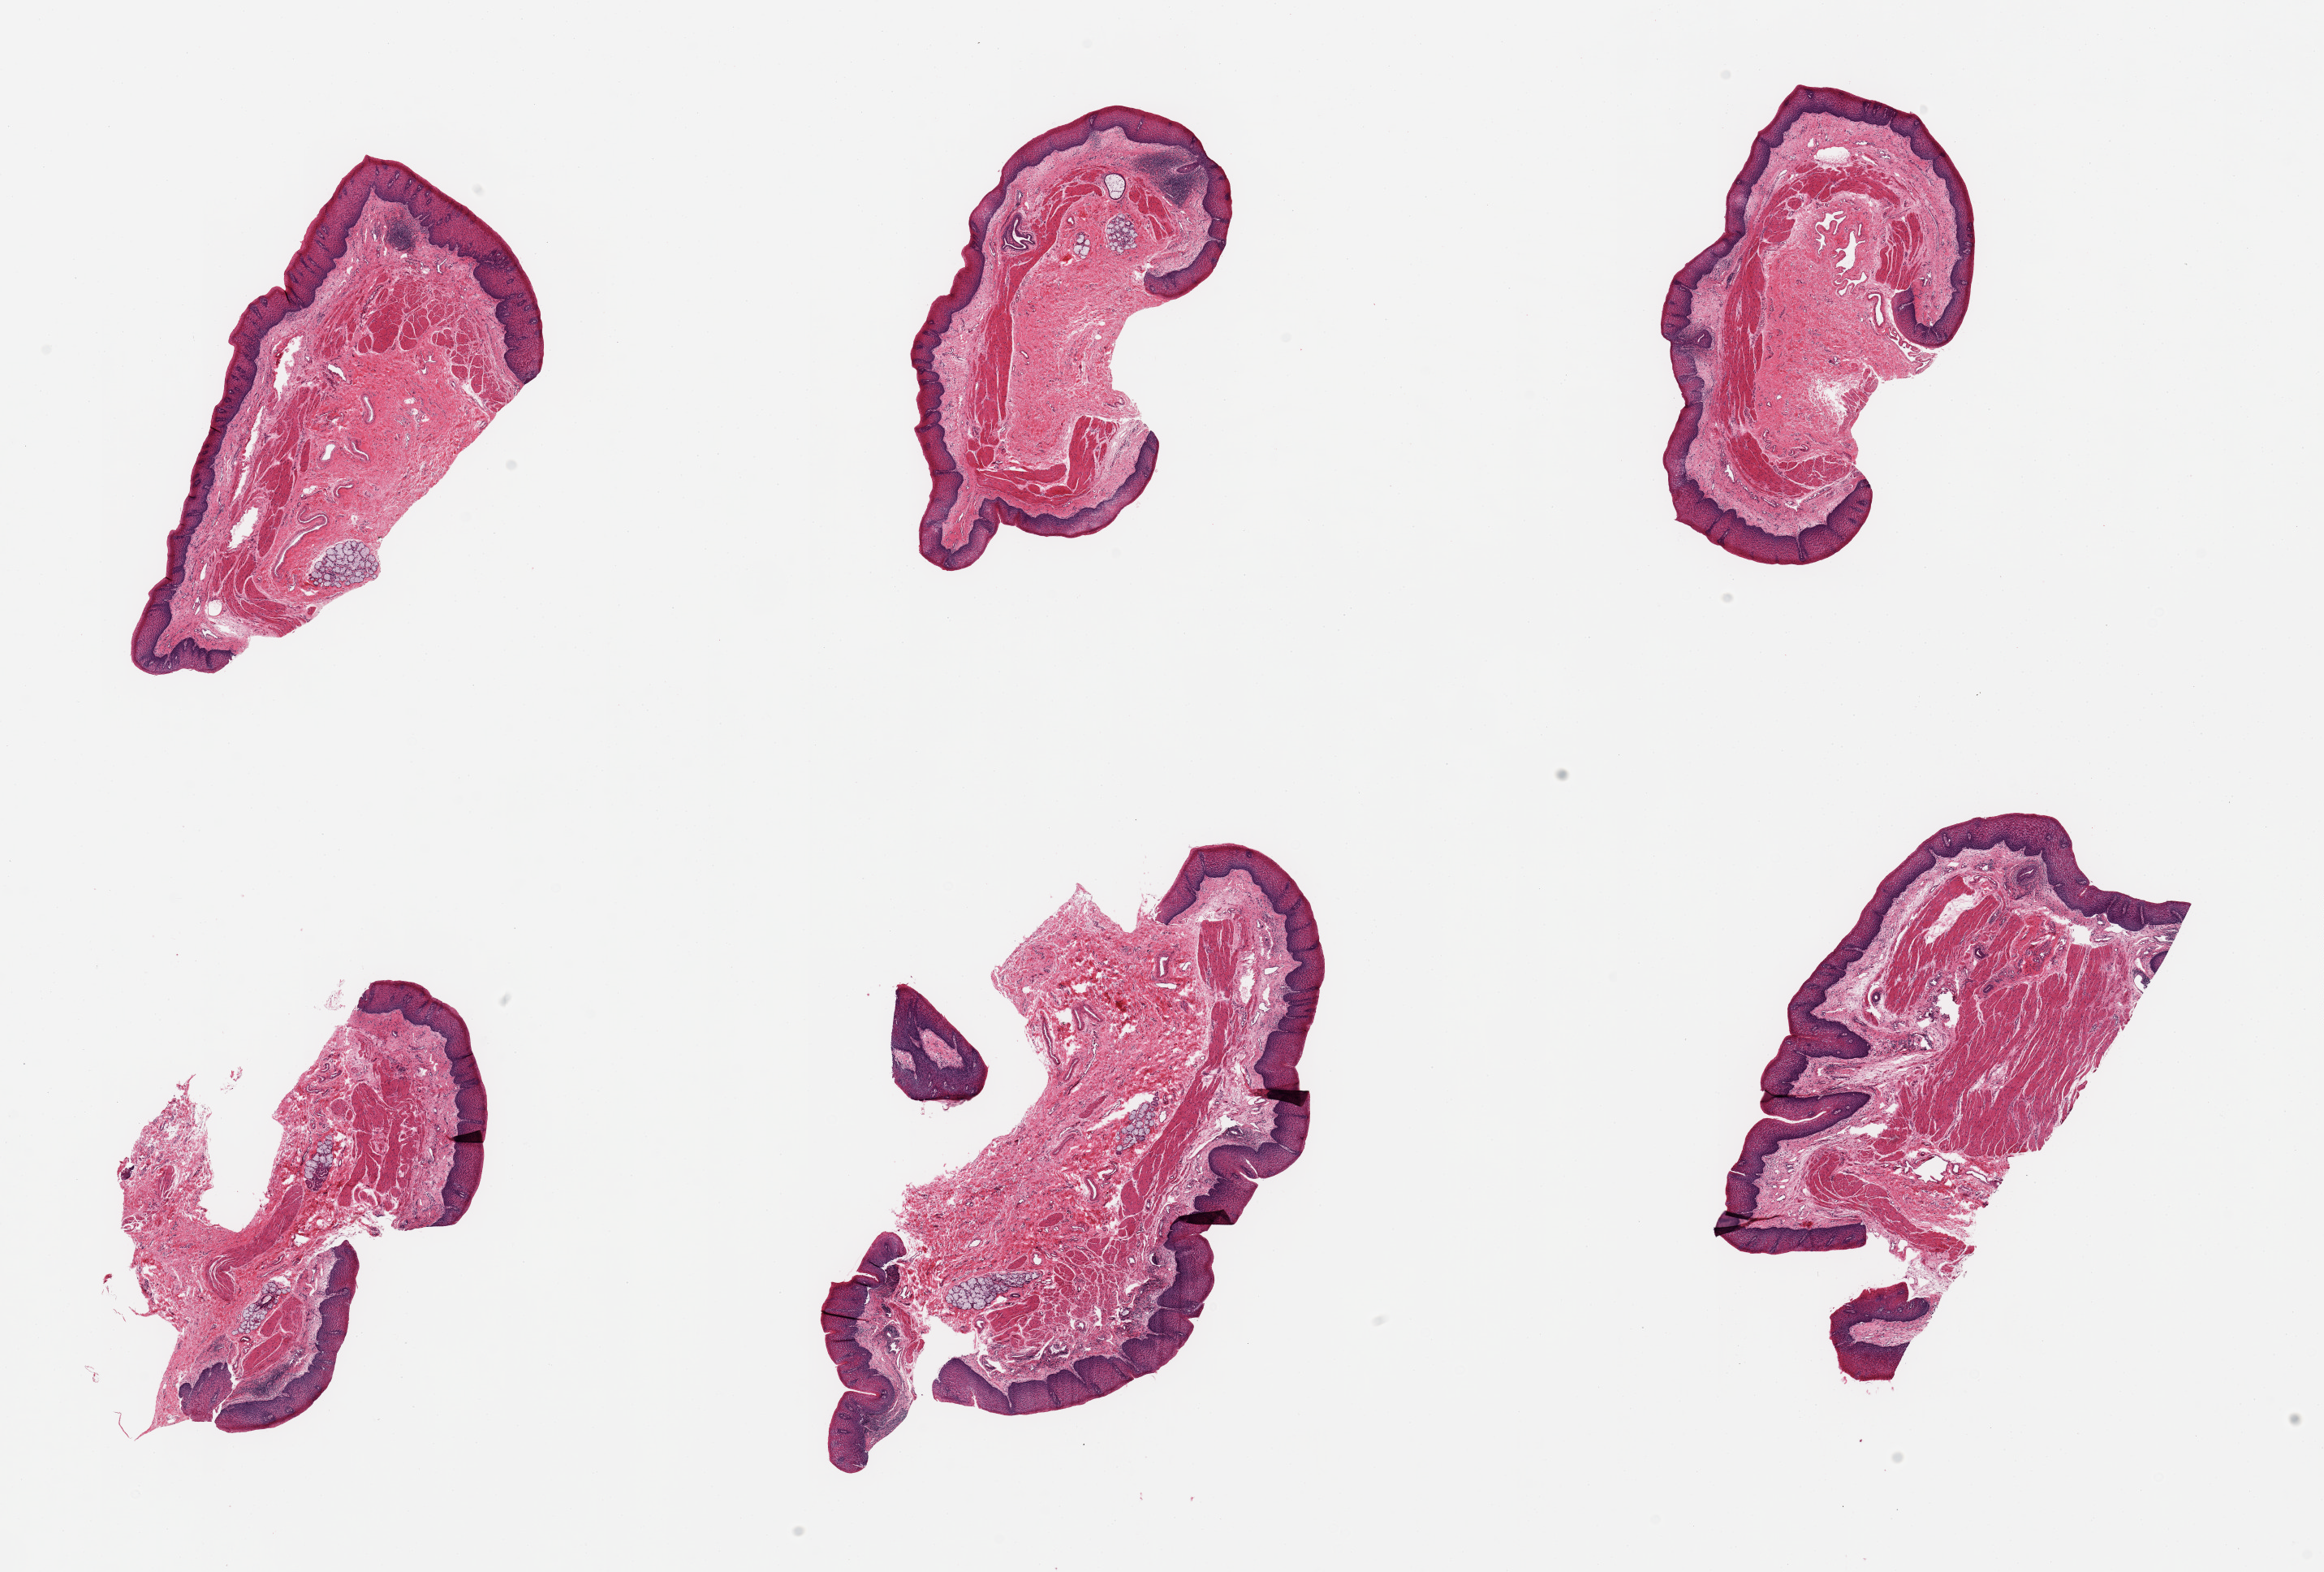
Whole-slide image, H&E stain, brightfield, a low-resolution overview of the entire scanned area, about 22.6 x 15.3 mm (acquisition: 20x scan). PAXgene-fixed, paraffin-embedded tissue. Section of esophageal mucous membrane (target tissue). Tissue donor sample. Donor: female.
Reviewer comment on this tissue sample: 6 pieces; target squamus mucosa and muscularis with submucosal glands in 4 of 6 pieces.